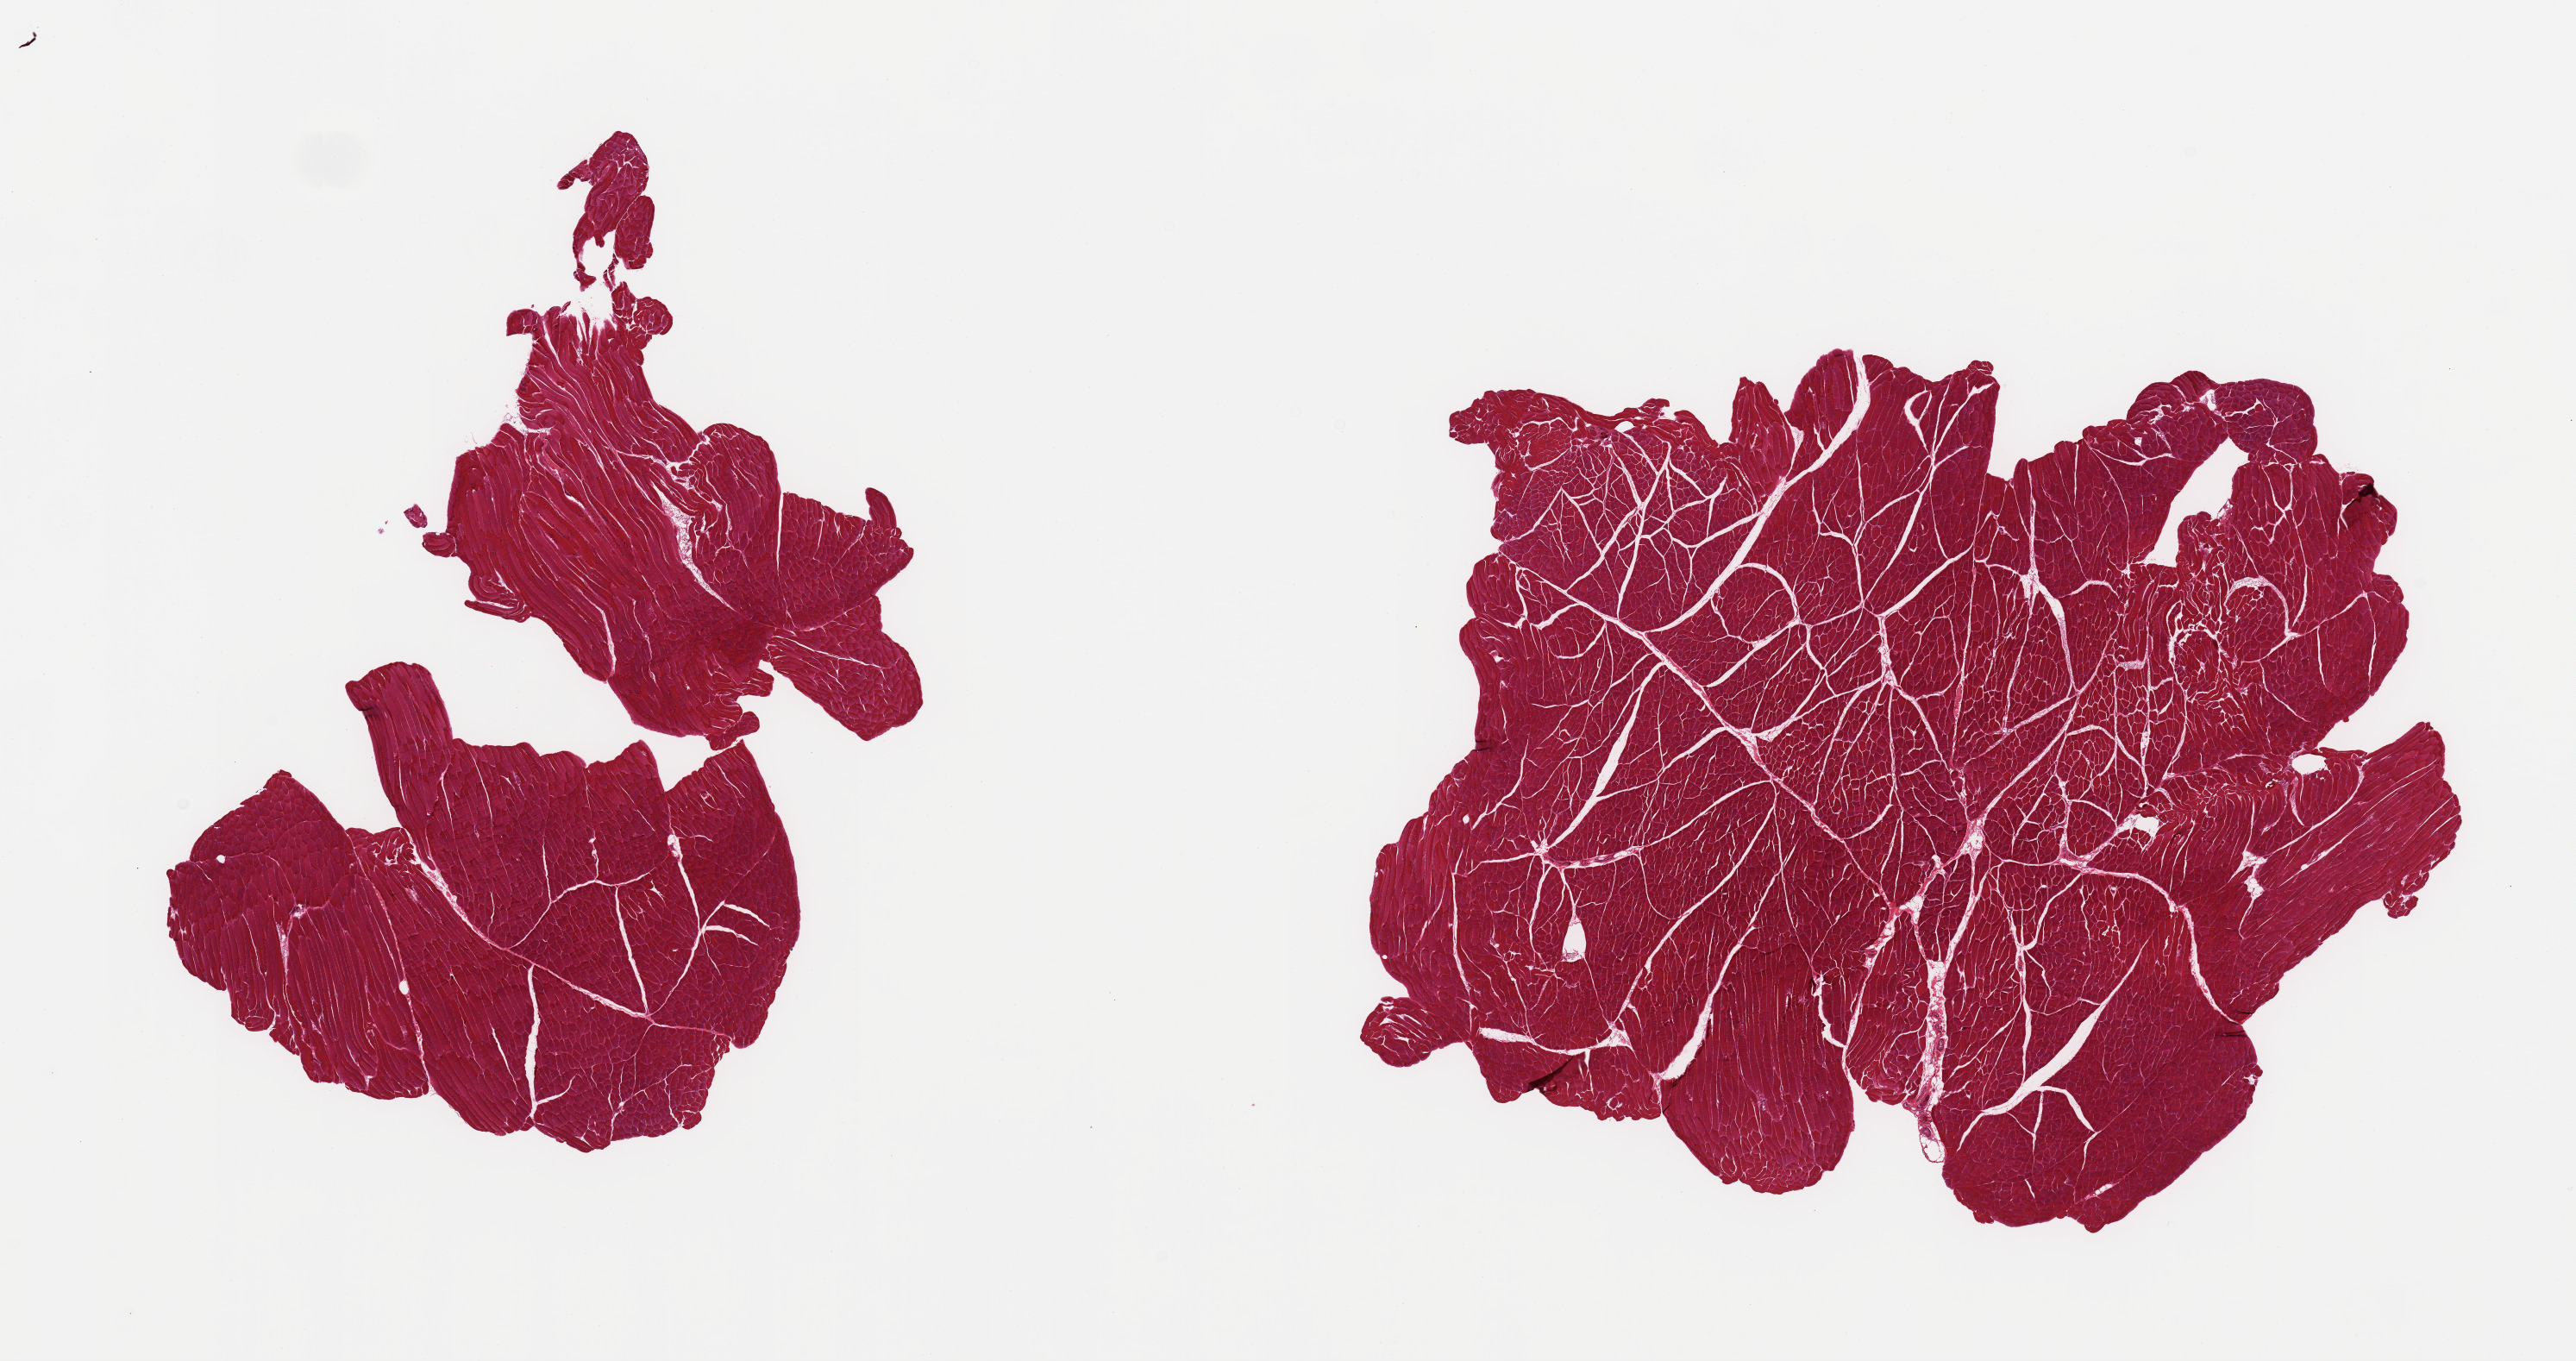
Digitized H&E-stained section — whole scanned area (about 23.6 x 12.5 mm, slide scanned at 20x) shown as a low-resolution overview. PAXgene-fixed, paraffin-embedded tissue. Section of skeletal muscle (target tissue). Tissue donor sample. Female donor.
Review note (as recorded): 2 pieces, ~5% interstitial fat/vascular elements.